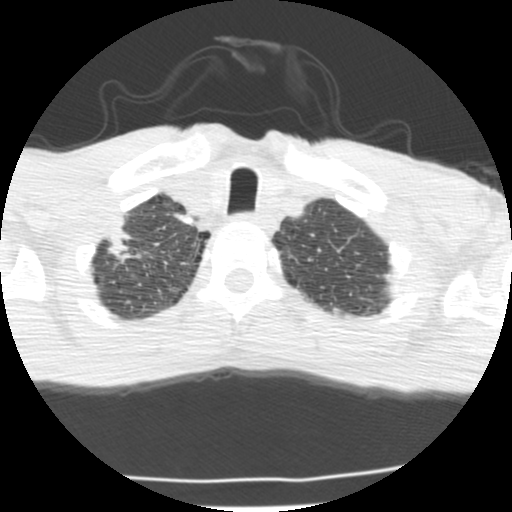
Low-dose screening chest CT, one axial slice; slice 190 of 214 in the series (ordered by position); reconstruction kernel STANDARD; lung window (W 1500 / L -600 HU); 512 × 512 image matrix, field of view 283 × 283 mm.
Structures marked on this image (expert manual segmentation):
- lesion 1 (tumor, upper lobe of right lung): bounding box [x1, y1, x2, y2] px = [105, 220, 132, 260]